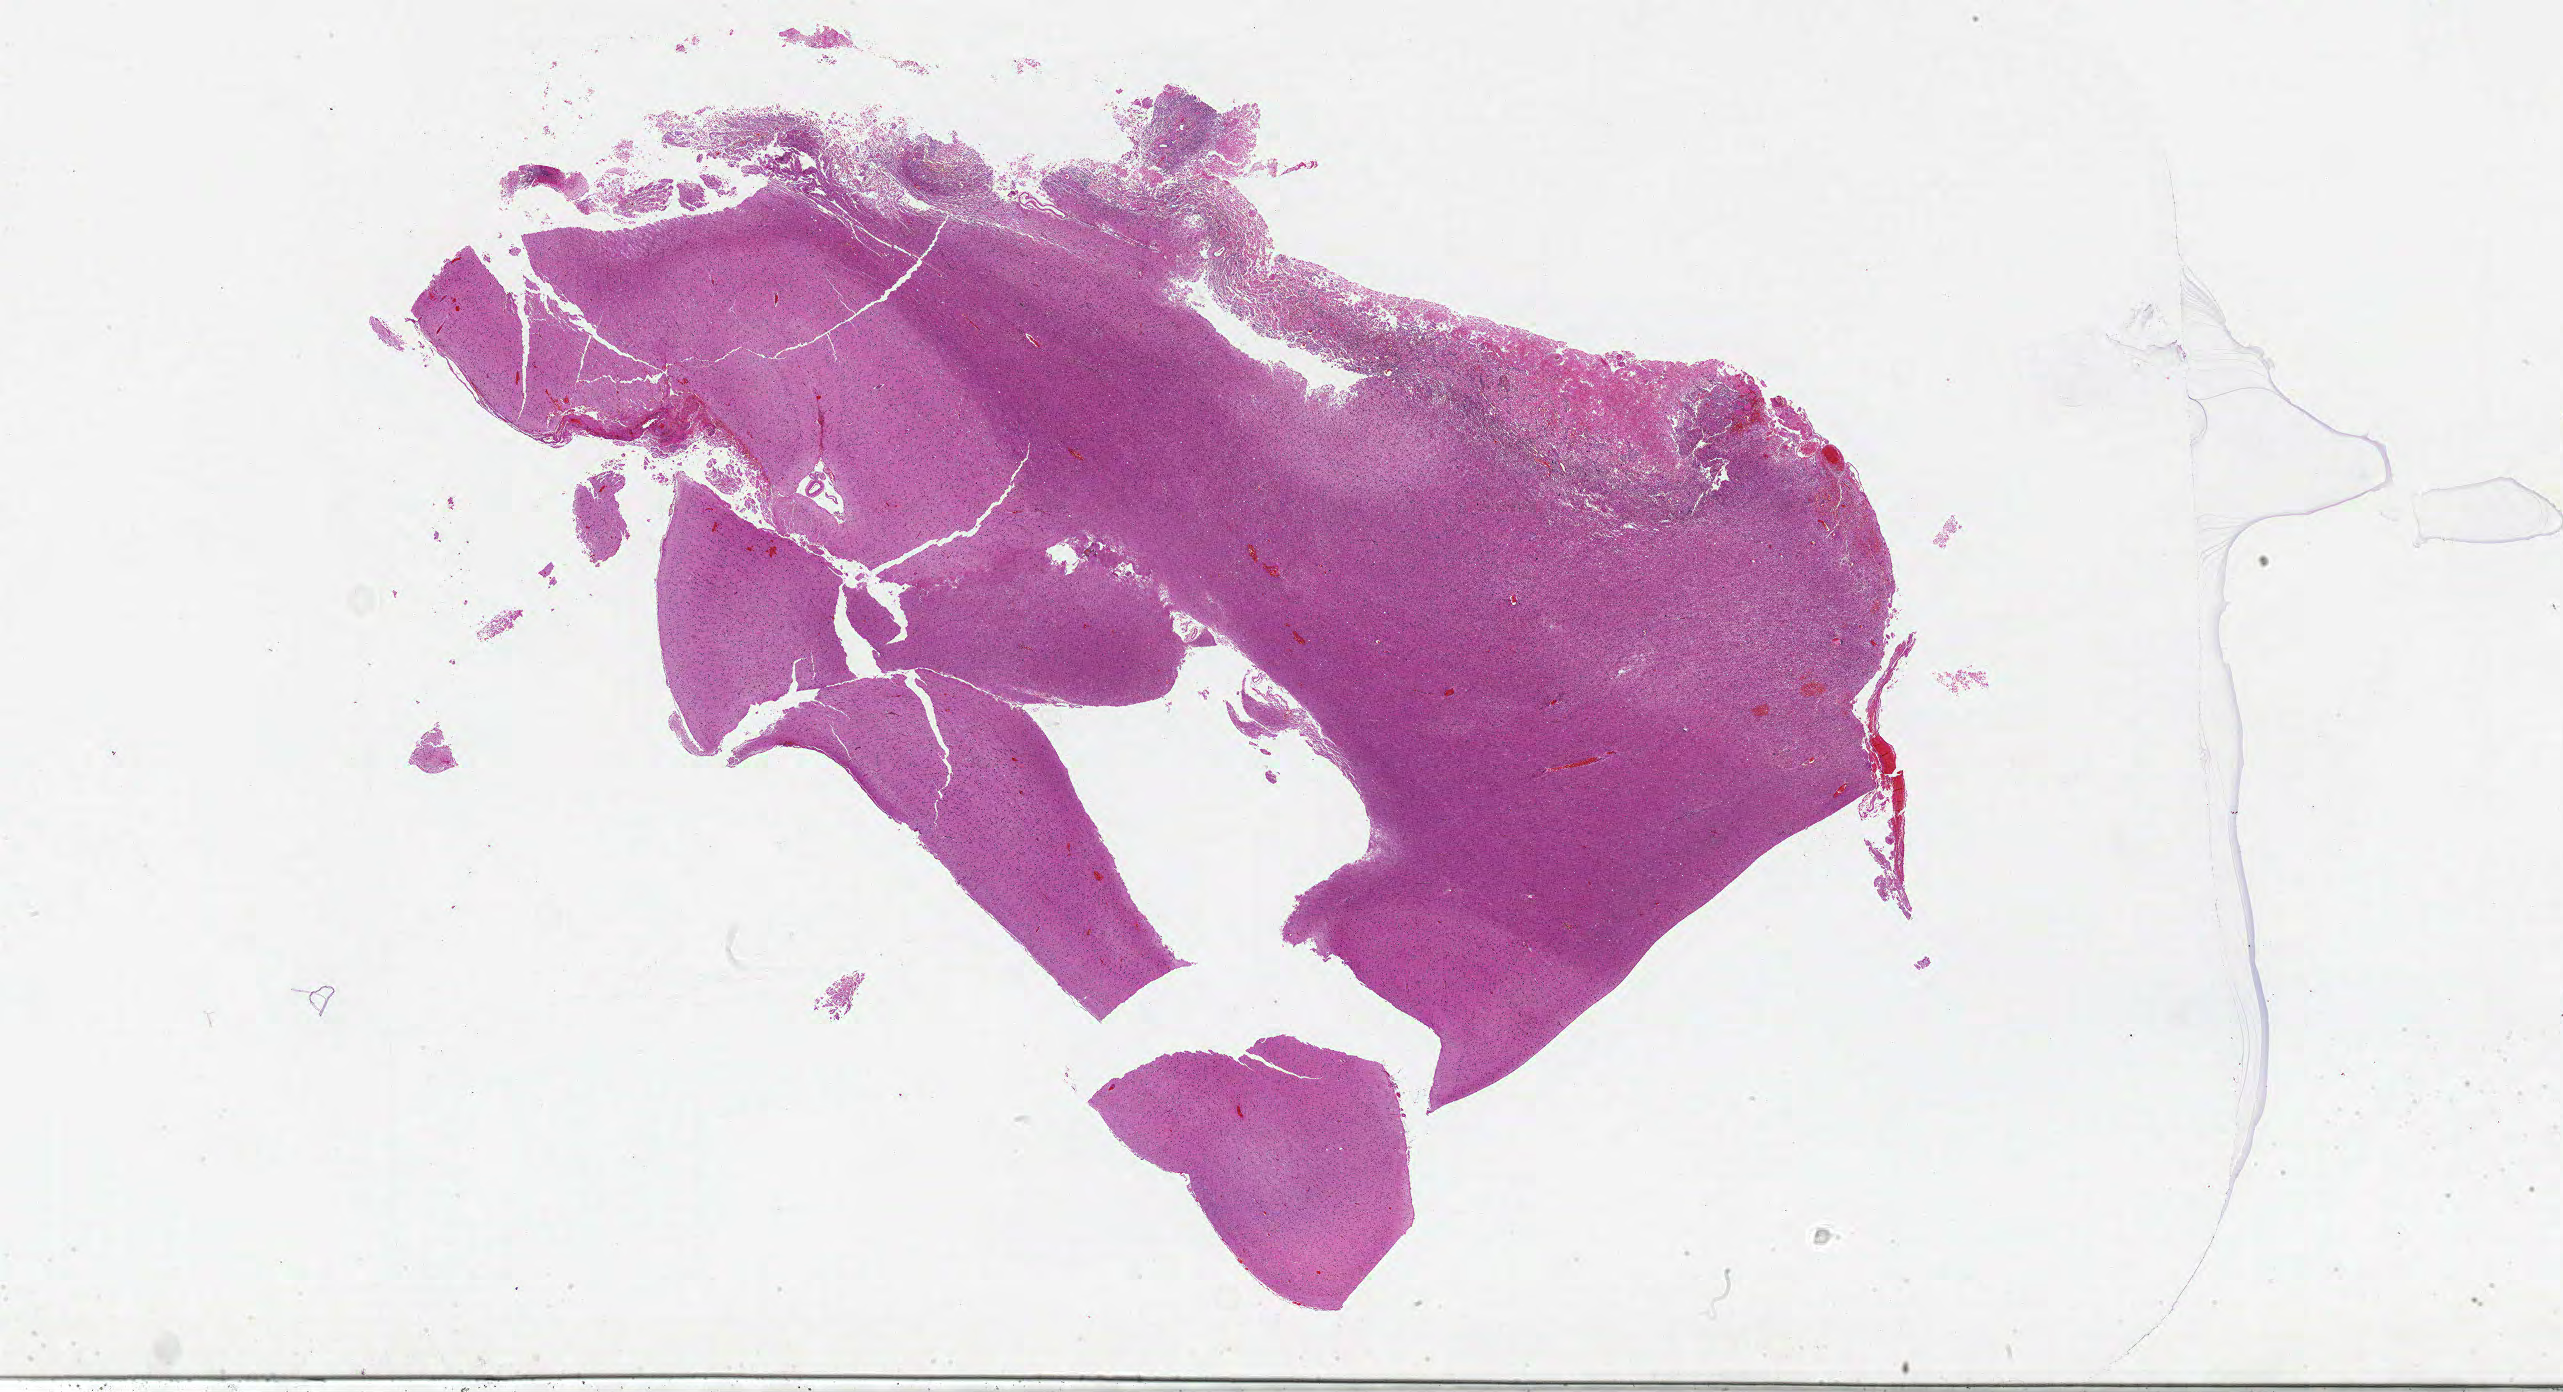
Digitized Hematoxylin and eosin (H&E) stained tissue section (whole slide) — whole scanned area (about 41.0 x 22.2 mm, slide scanned at 20x) shown as a low-resolution overview, formalin-fixed paraffin-embedded (FFPE) diagnostic section, sample: primary tumour, brain. Male, age 55 years at initial diagnosis.
Histologic diagnosis: Glioblastoma.